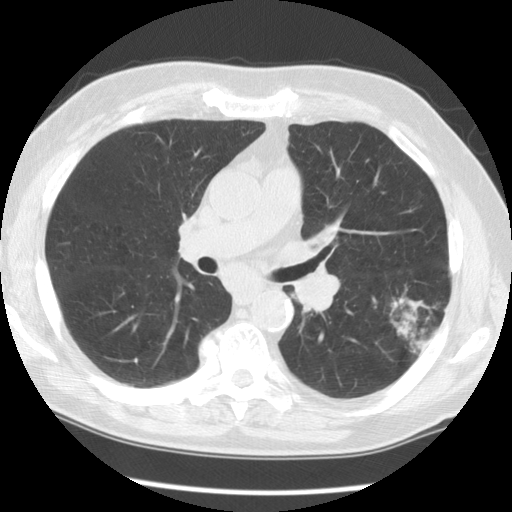
Low-dose screening chest CT, one axial slice. Position 78 of 130 along the scan axis. 120 kVp. Lung window (W 1500 / L -600 HU). 2.5 mm slice thickness. 512 × 512 image matrix, field of view 340 × 340 mm.
Structures marked on this image (outlined manually by an expert reader):
- lesion 1 (tumor, lower lobe of left lung): bounding box [x1, y1, x2, y2] px = [390, 298, 437, 353]